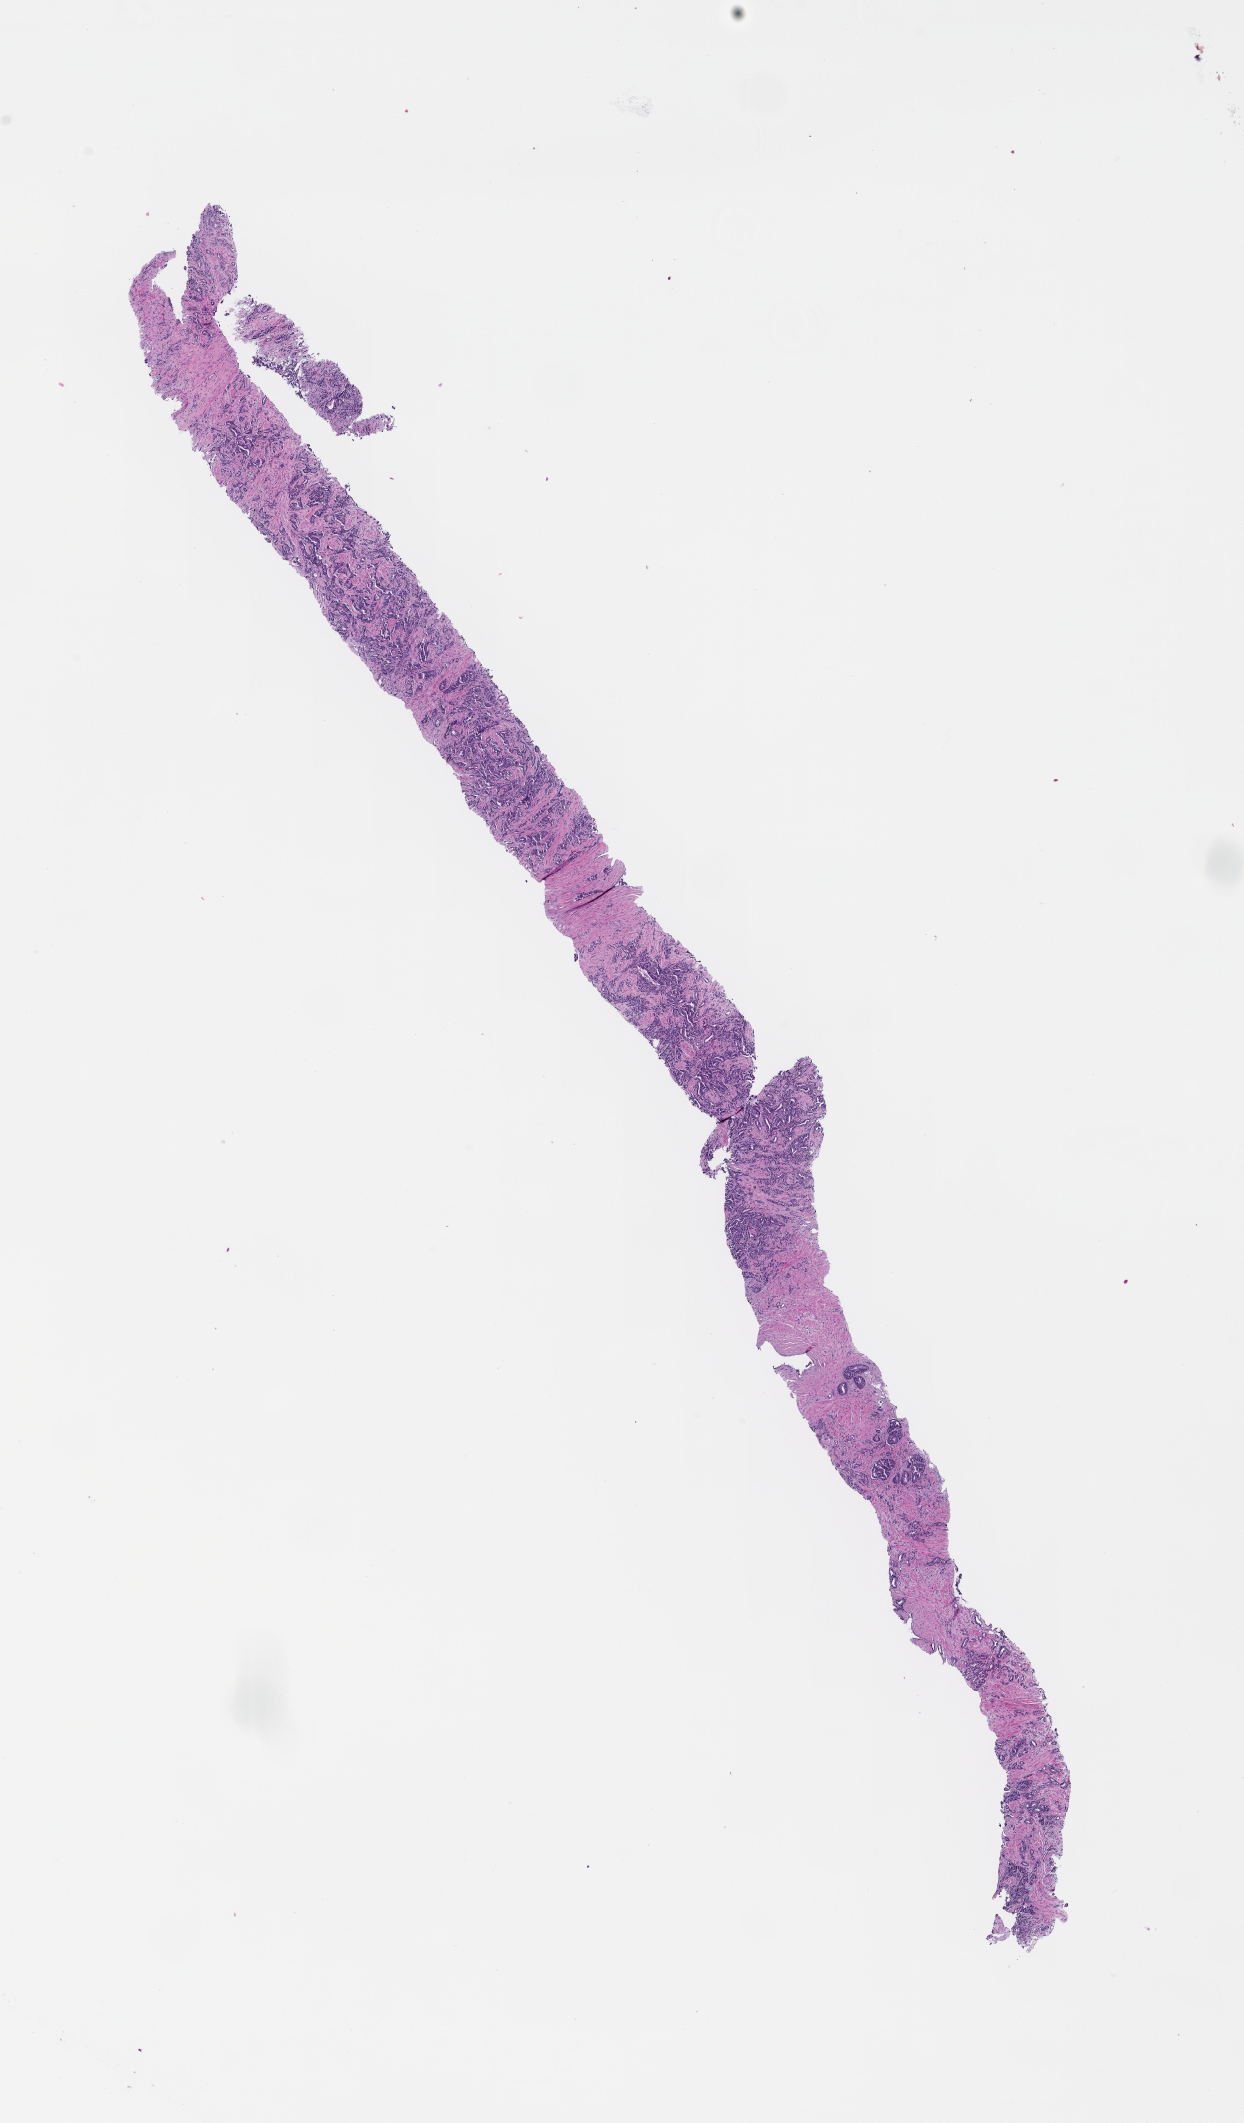
Digitized hematoxylin and eosin (H&E)-stained section — a low-resolution overview of the entire scanned area, about 10.1 x 17.2 mm; FFPE section; site: prostate; archival tissue. Male patient.
This section: primary tumour tissue. Diagnosis: Prostate Carcinoma.